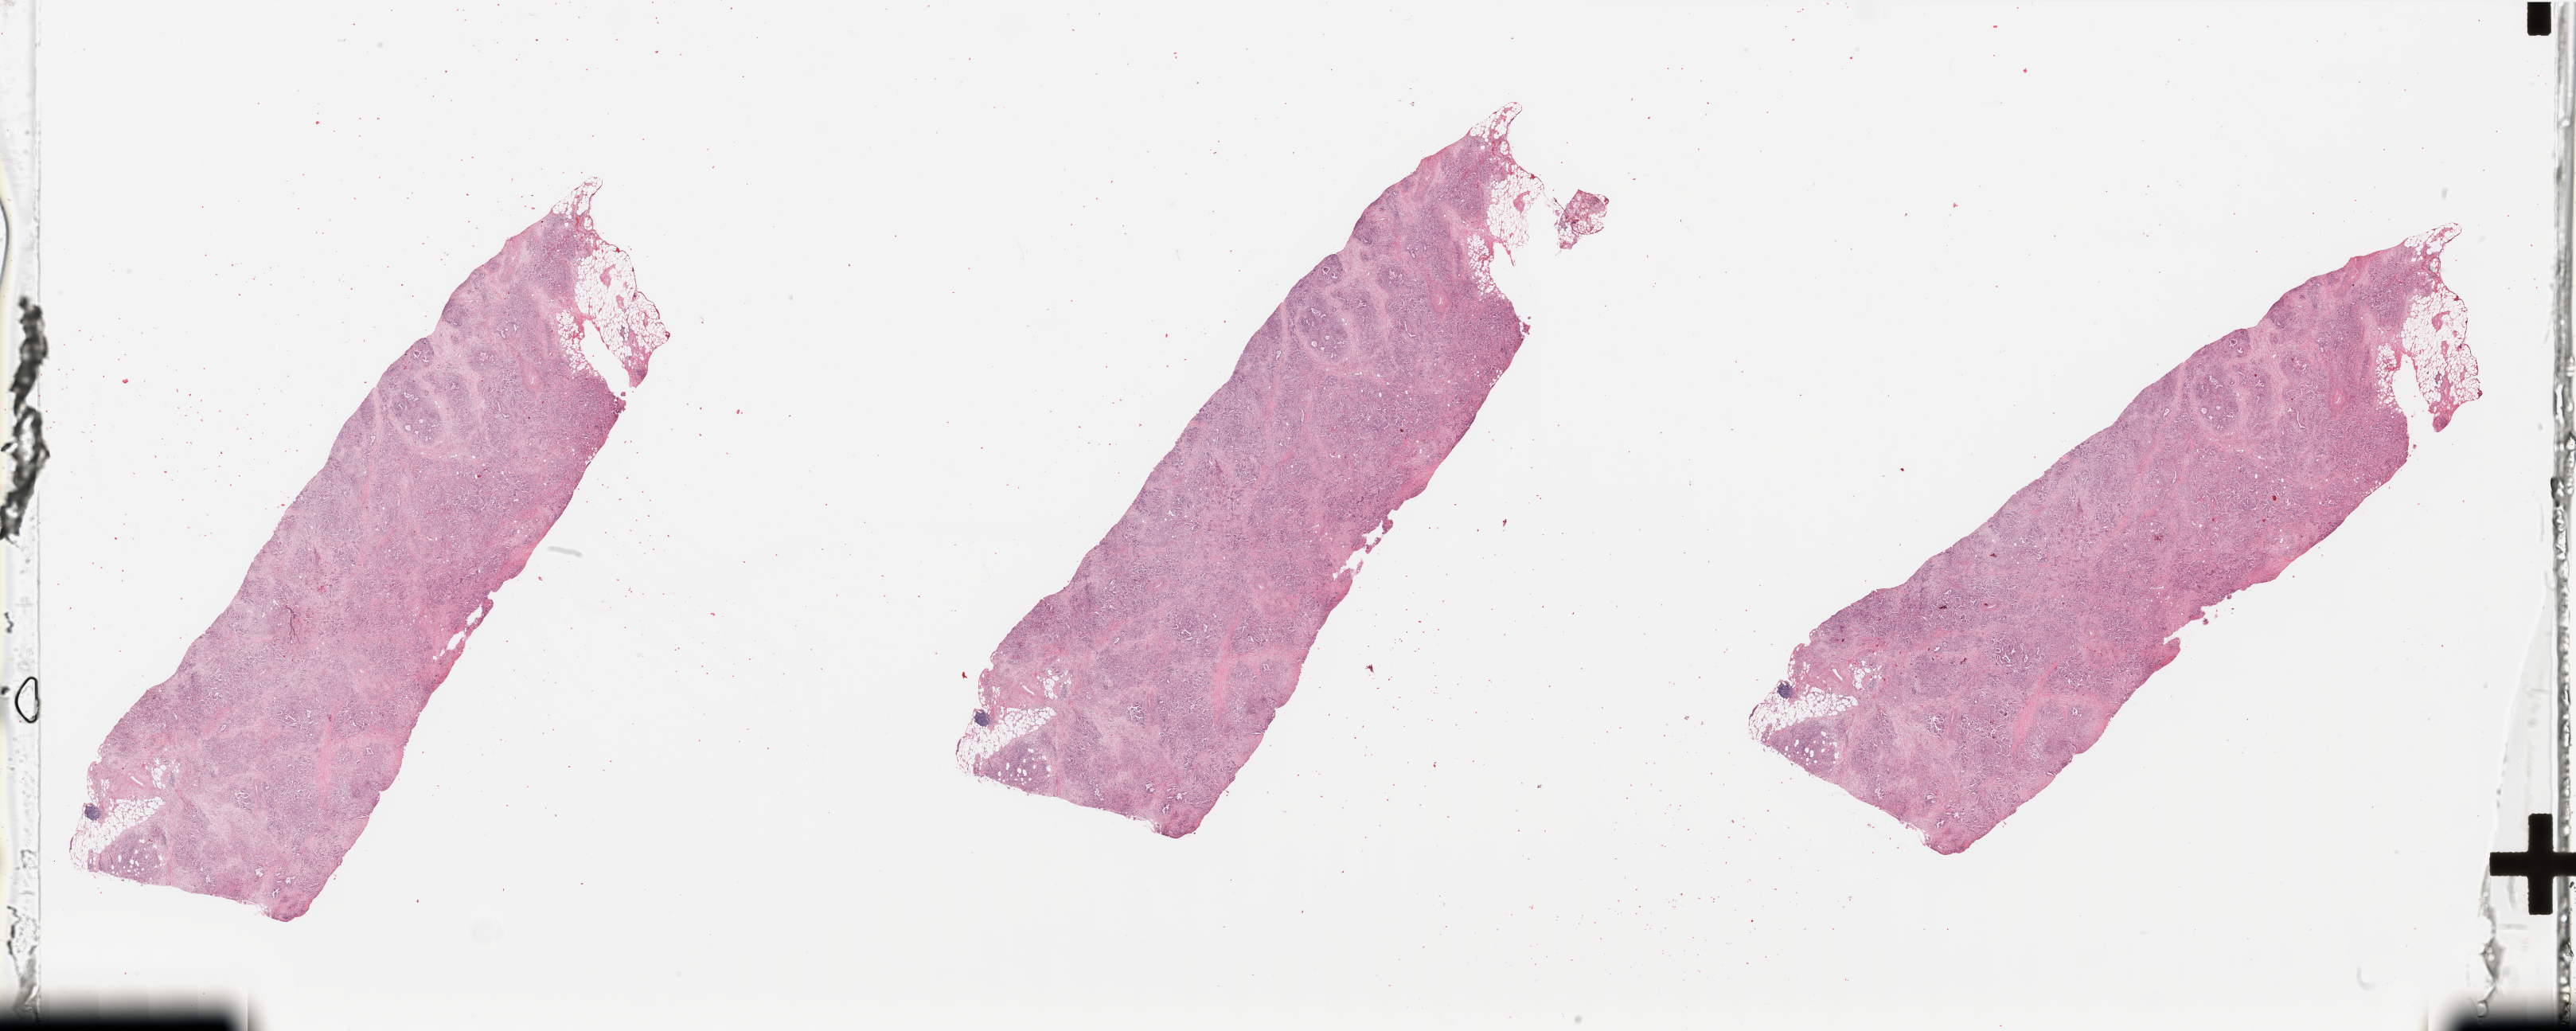
Digitized H&E tissue section (whole slide), whole scanned area (about 51.2 x 20.5 mm, from a 20x scan) shown as a low-resolution overview, tumour tissue sample, pancreas. Patient: male, age 84 years.
Patient diagnosis (cohort enrolment): ductal adenocarcinoma (pancreas). Primary tumour site (as recorded): head.